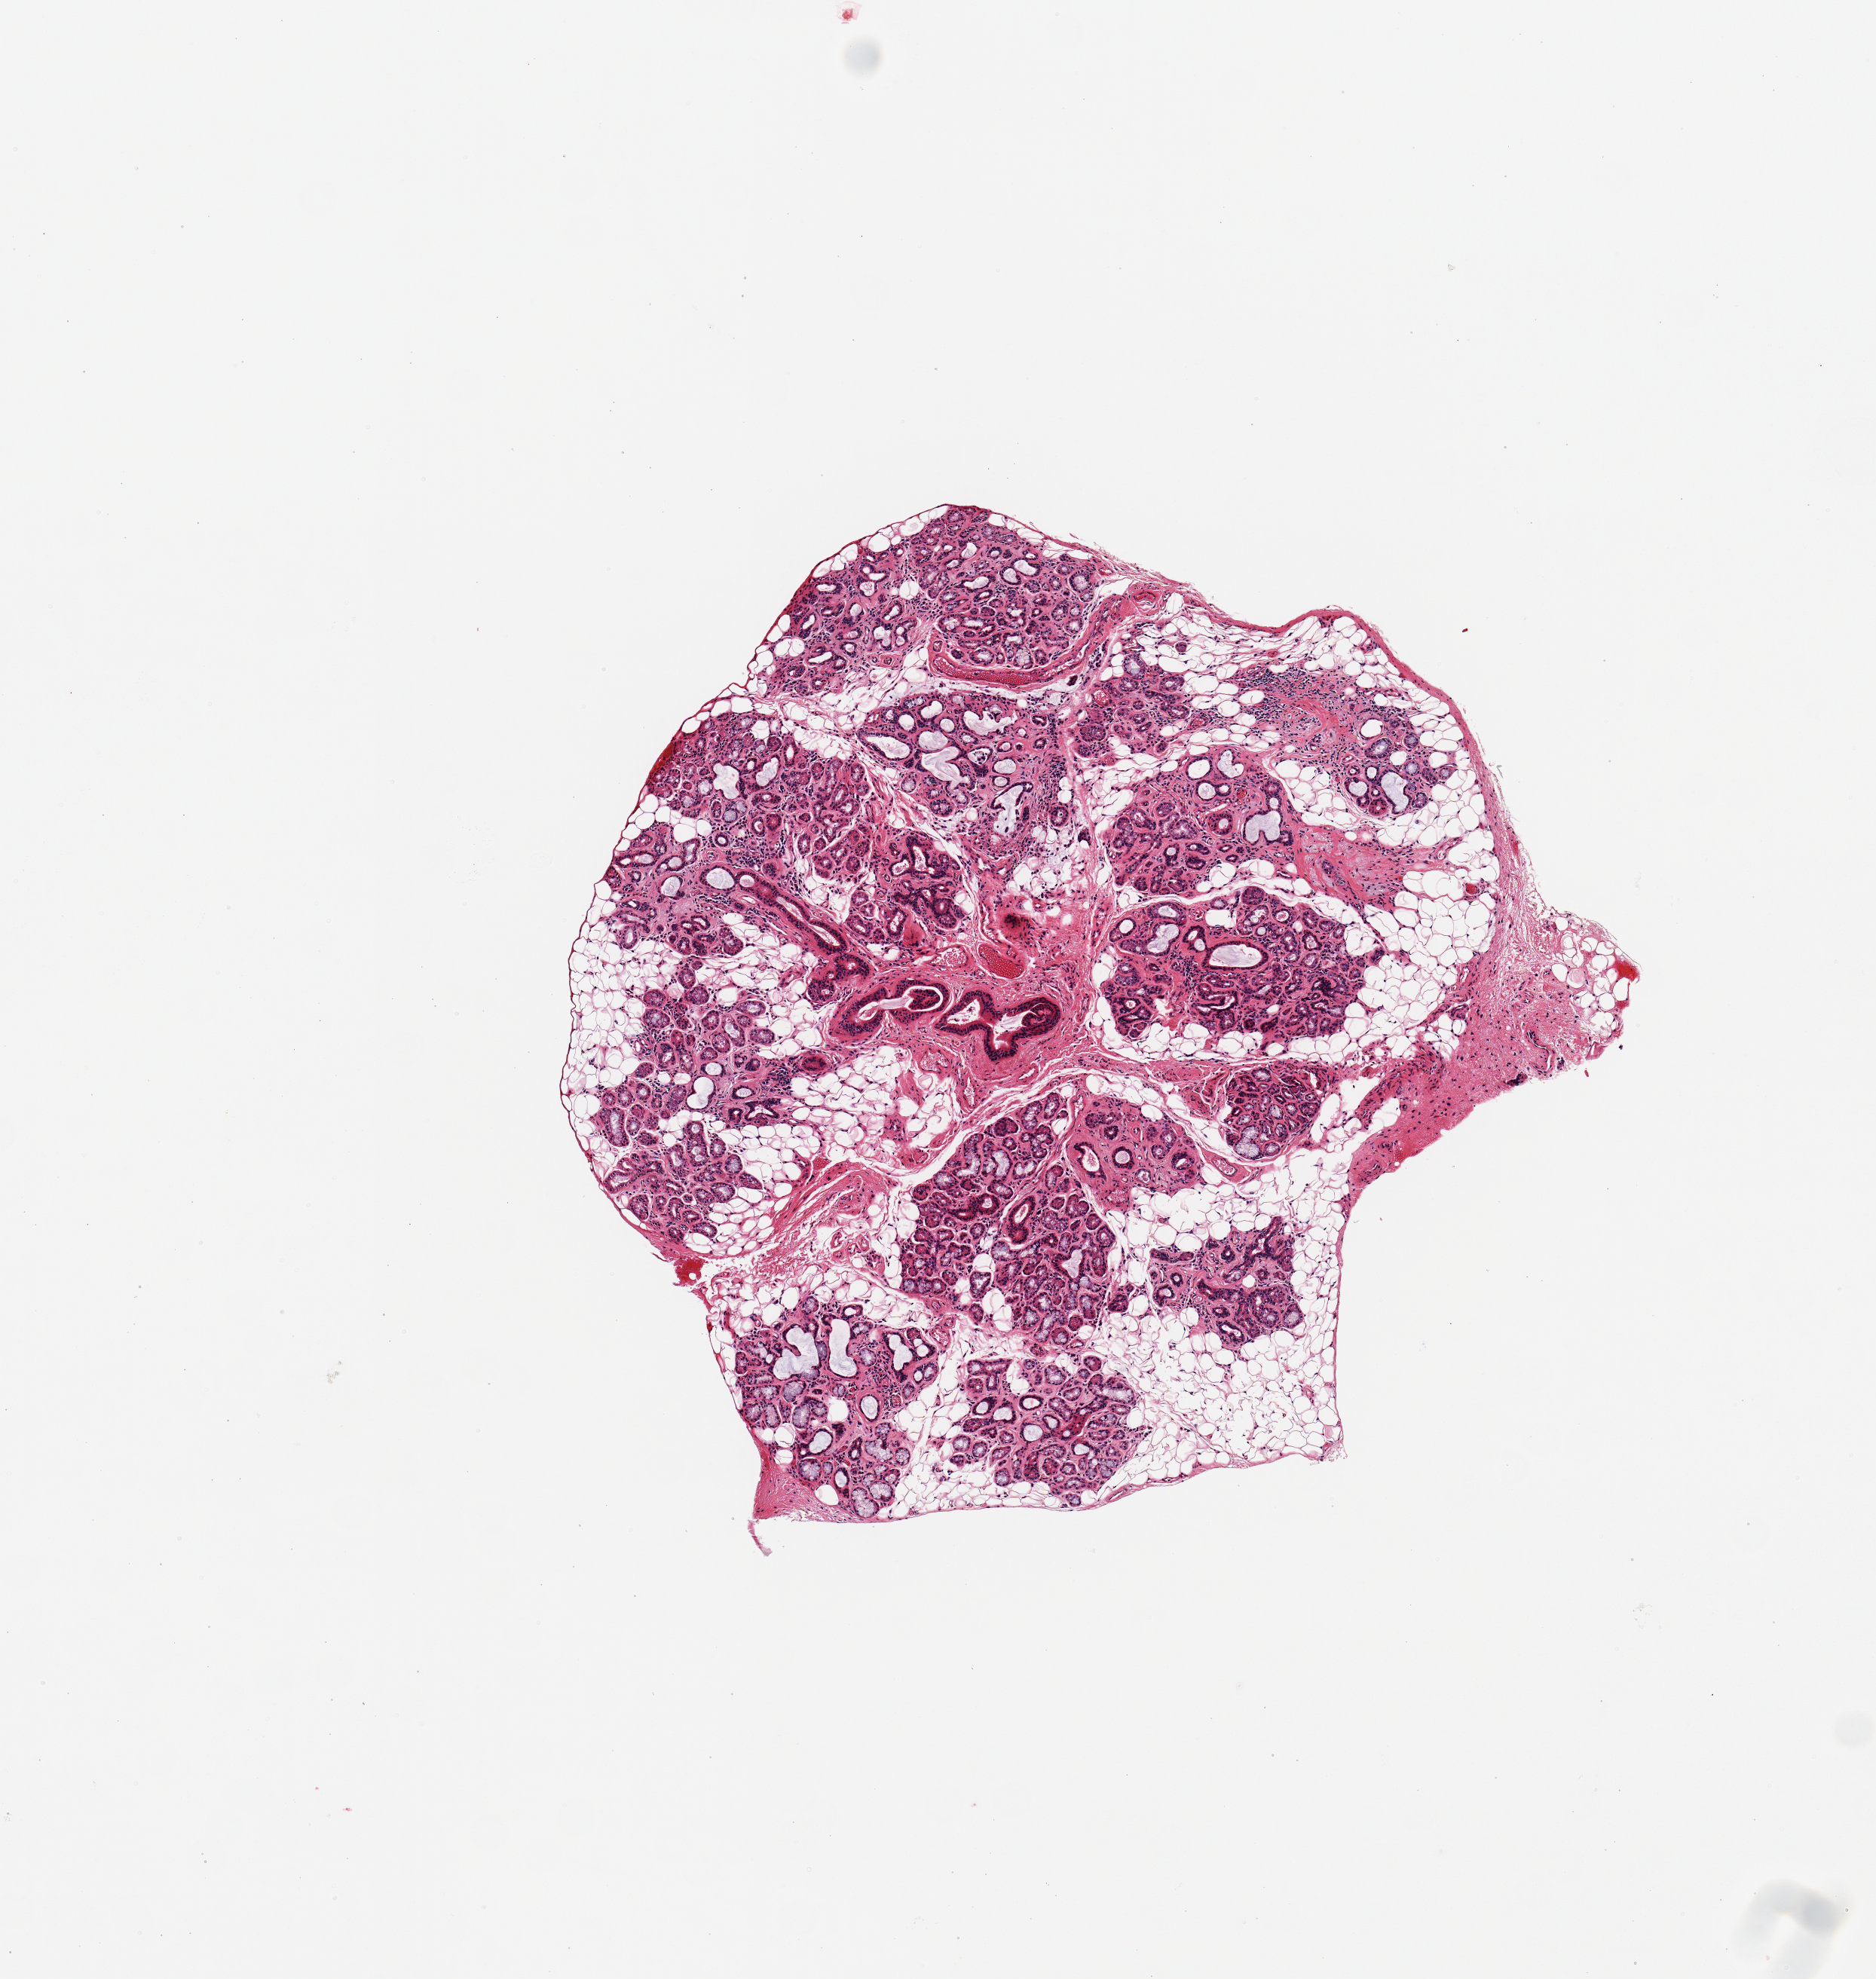
Digitized H&E-stained section, a low-resolution overview of the entire scanned area, about 4.9 x 5.2 mm (slide scanned at 20x). PAXgene-fixed paraffin-embedded (PFPE) section. Sampled site (target tissue): minor salivary gland. Donor tissue sample.
Reviewer comment on this tissue sample: 1 piece, ~60% glandular elements, rest is interstitial/adherent fat; Evidence of remote sialadenitis with scarring.